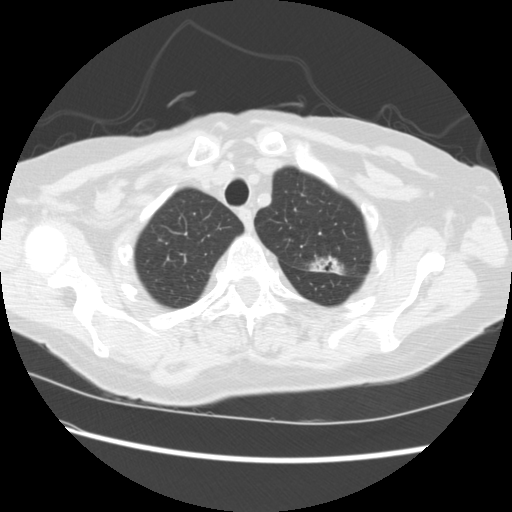
Chest CT (low-dose screening protocol), one axial image. Baseline annual screen. Lung window (W 1500 / L -600 HU). Slice 38 of 224 in the series. 512 × 512 image matrix, field of view 340 × 340 mm. Female, age 74 years at enrolment. Former smoker at enrolment.
- Expert reader's lesion annotation, bounding box (x1, y1, x2, y2) in pixels: (297, 247, 347, 285).
- The screening reader recorded 2 non-calcified nodules or masses ≥4 mm on this exam (left upper lobe, right lower lobe); which of them this box marks is not recorded.
- Official screen result: positive, change unspecified: nodule(s) >= 4 mm or enlarging nodule(s), mass(es), or other non-specific abnormalities suspicious for lung cancer.
- Participant outcome: lung cancer diagnosed 309 days after this screen — non-small cell carcinoma, left upper lobe, stage IV (AJCC 6th edition).